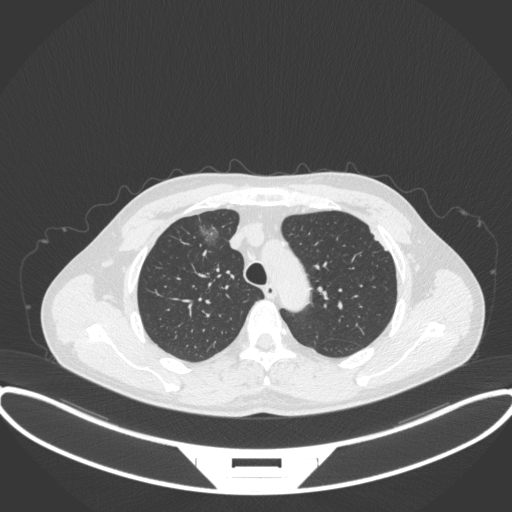
Chest CT, one axial slice; position 277 of 395 along the scan axis; reconstruction kernel B31f; 120 kVp; lung window (W 1500 / L -600 HU); 1 mm slice thickness; 512 × 512 image matrix, field of view 424 × 424 mm. Male patient, age 60 years. From the clinical record (not read from this slice): clinical TNM (as recorded): T1c N0 M0.
Structures marked on this image (rectangle marked by the reading radiologist):
- lung tumour (recorded histology: adenocarcinoma): box from (x=189, y=214) to (x=230, y=253) px